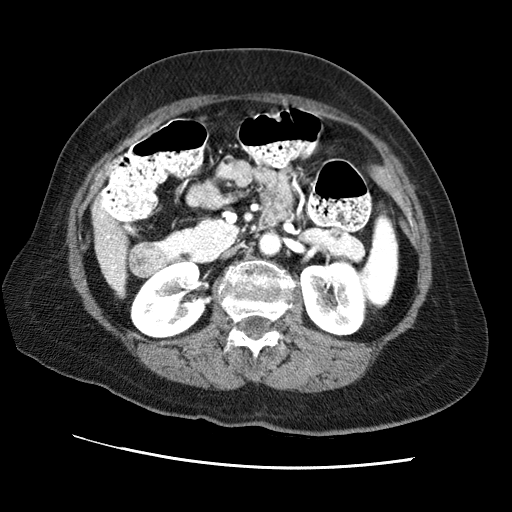
Contrast-enhanced abdominal CT (liver protocol), one axial slice; position 17 of 65 along the scan axis; soft-tissue window (W 400 / L 40 HU); 512 × 512 image matrix, field of view 340 × 340 mm. From the clinical record (not read from this slice): diagnosis: hepatocellular carcinoma (patient treated with transarterial chemoembolisation; whether this scan precedes or follows treatment is not stated here); TNM stage (as recorded): Stage-II.
Outlined on this slice (semi-automatic segmentation, software-assisted and operator-edited):
- liver parenchyma outside the tumour (the mass and vessels are separate outlines, so this box may not span the whole liver): box from (x=94, y=212) to (x=126, y=294) px
- liver vessels: (x=101, y=214)–(x=123, y=290)